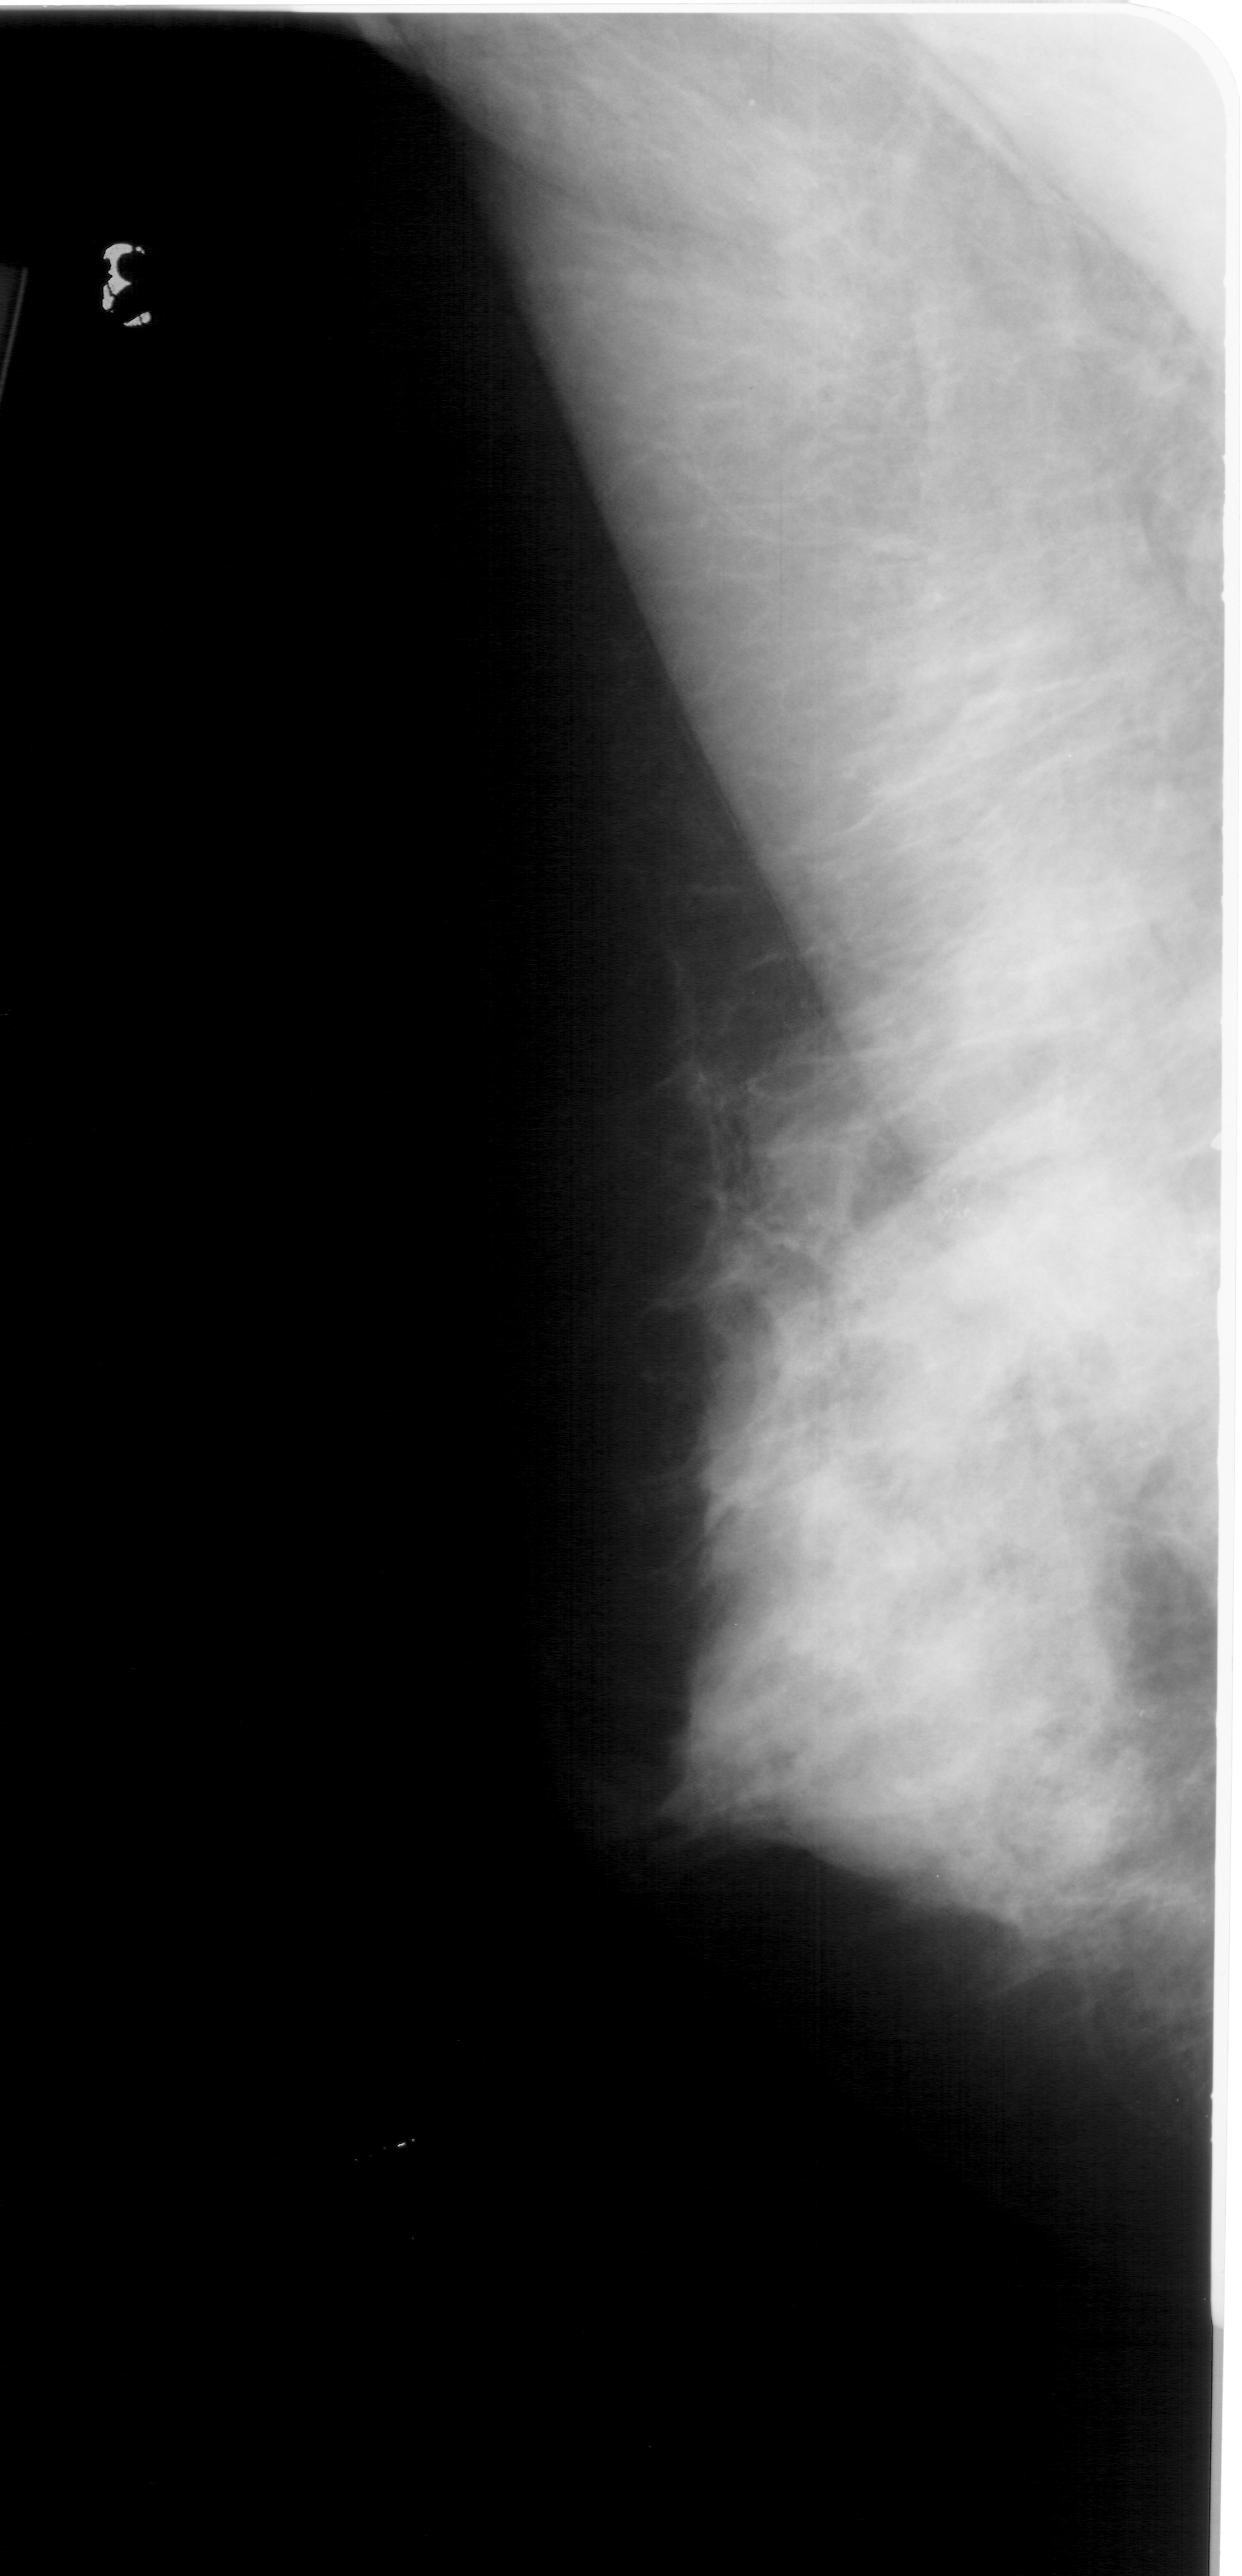
Scanned film-screen mammogram; left breast; mediolateral oblique (MLO) view; 1242 × 2576 image matrix.
Expert-marked regions of interest on this image (one box per marked abnormality):
- mass, shape irregular, margins ill defined; BI-RADS assessment category 4; subtlety rating 3 on a 1 (subtle) to 5 (obvious) scale; pathology (as recorded): malignant: bounding box (x1, y1, x2, y2) in pixels: (921, 1176, 1109, 1375)